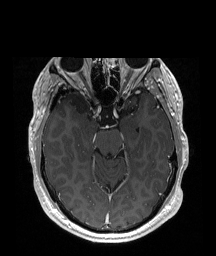
Brain MRI from a brain-tumour surgery series, one axial slice. Position 123 of 192 along the scan axis. T1-weighted post-contrast. 1 mm slice thickness. 216 × 256 image matrix. From the clinical record (not read from this slice): histopathology: Astrocytoma; WHO grade: 2; IDH mutation: yes.
Annotated regions visible in this slice (outlined manually by an expert reader):
- tumour: box from (x=69, y=92) to (x=90, y=120) px